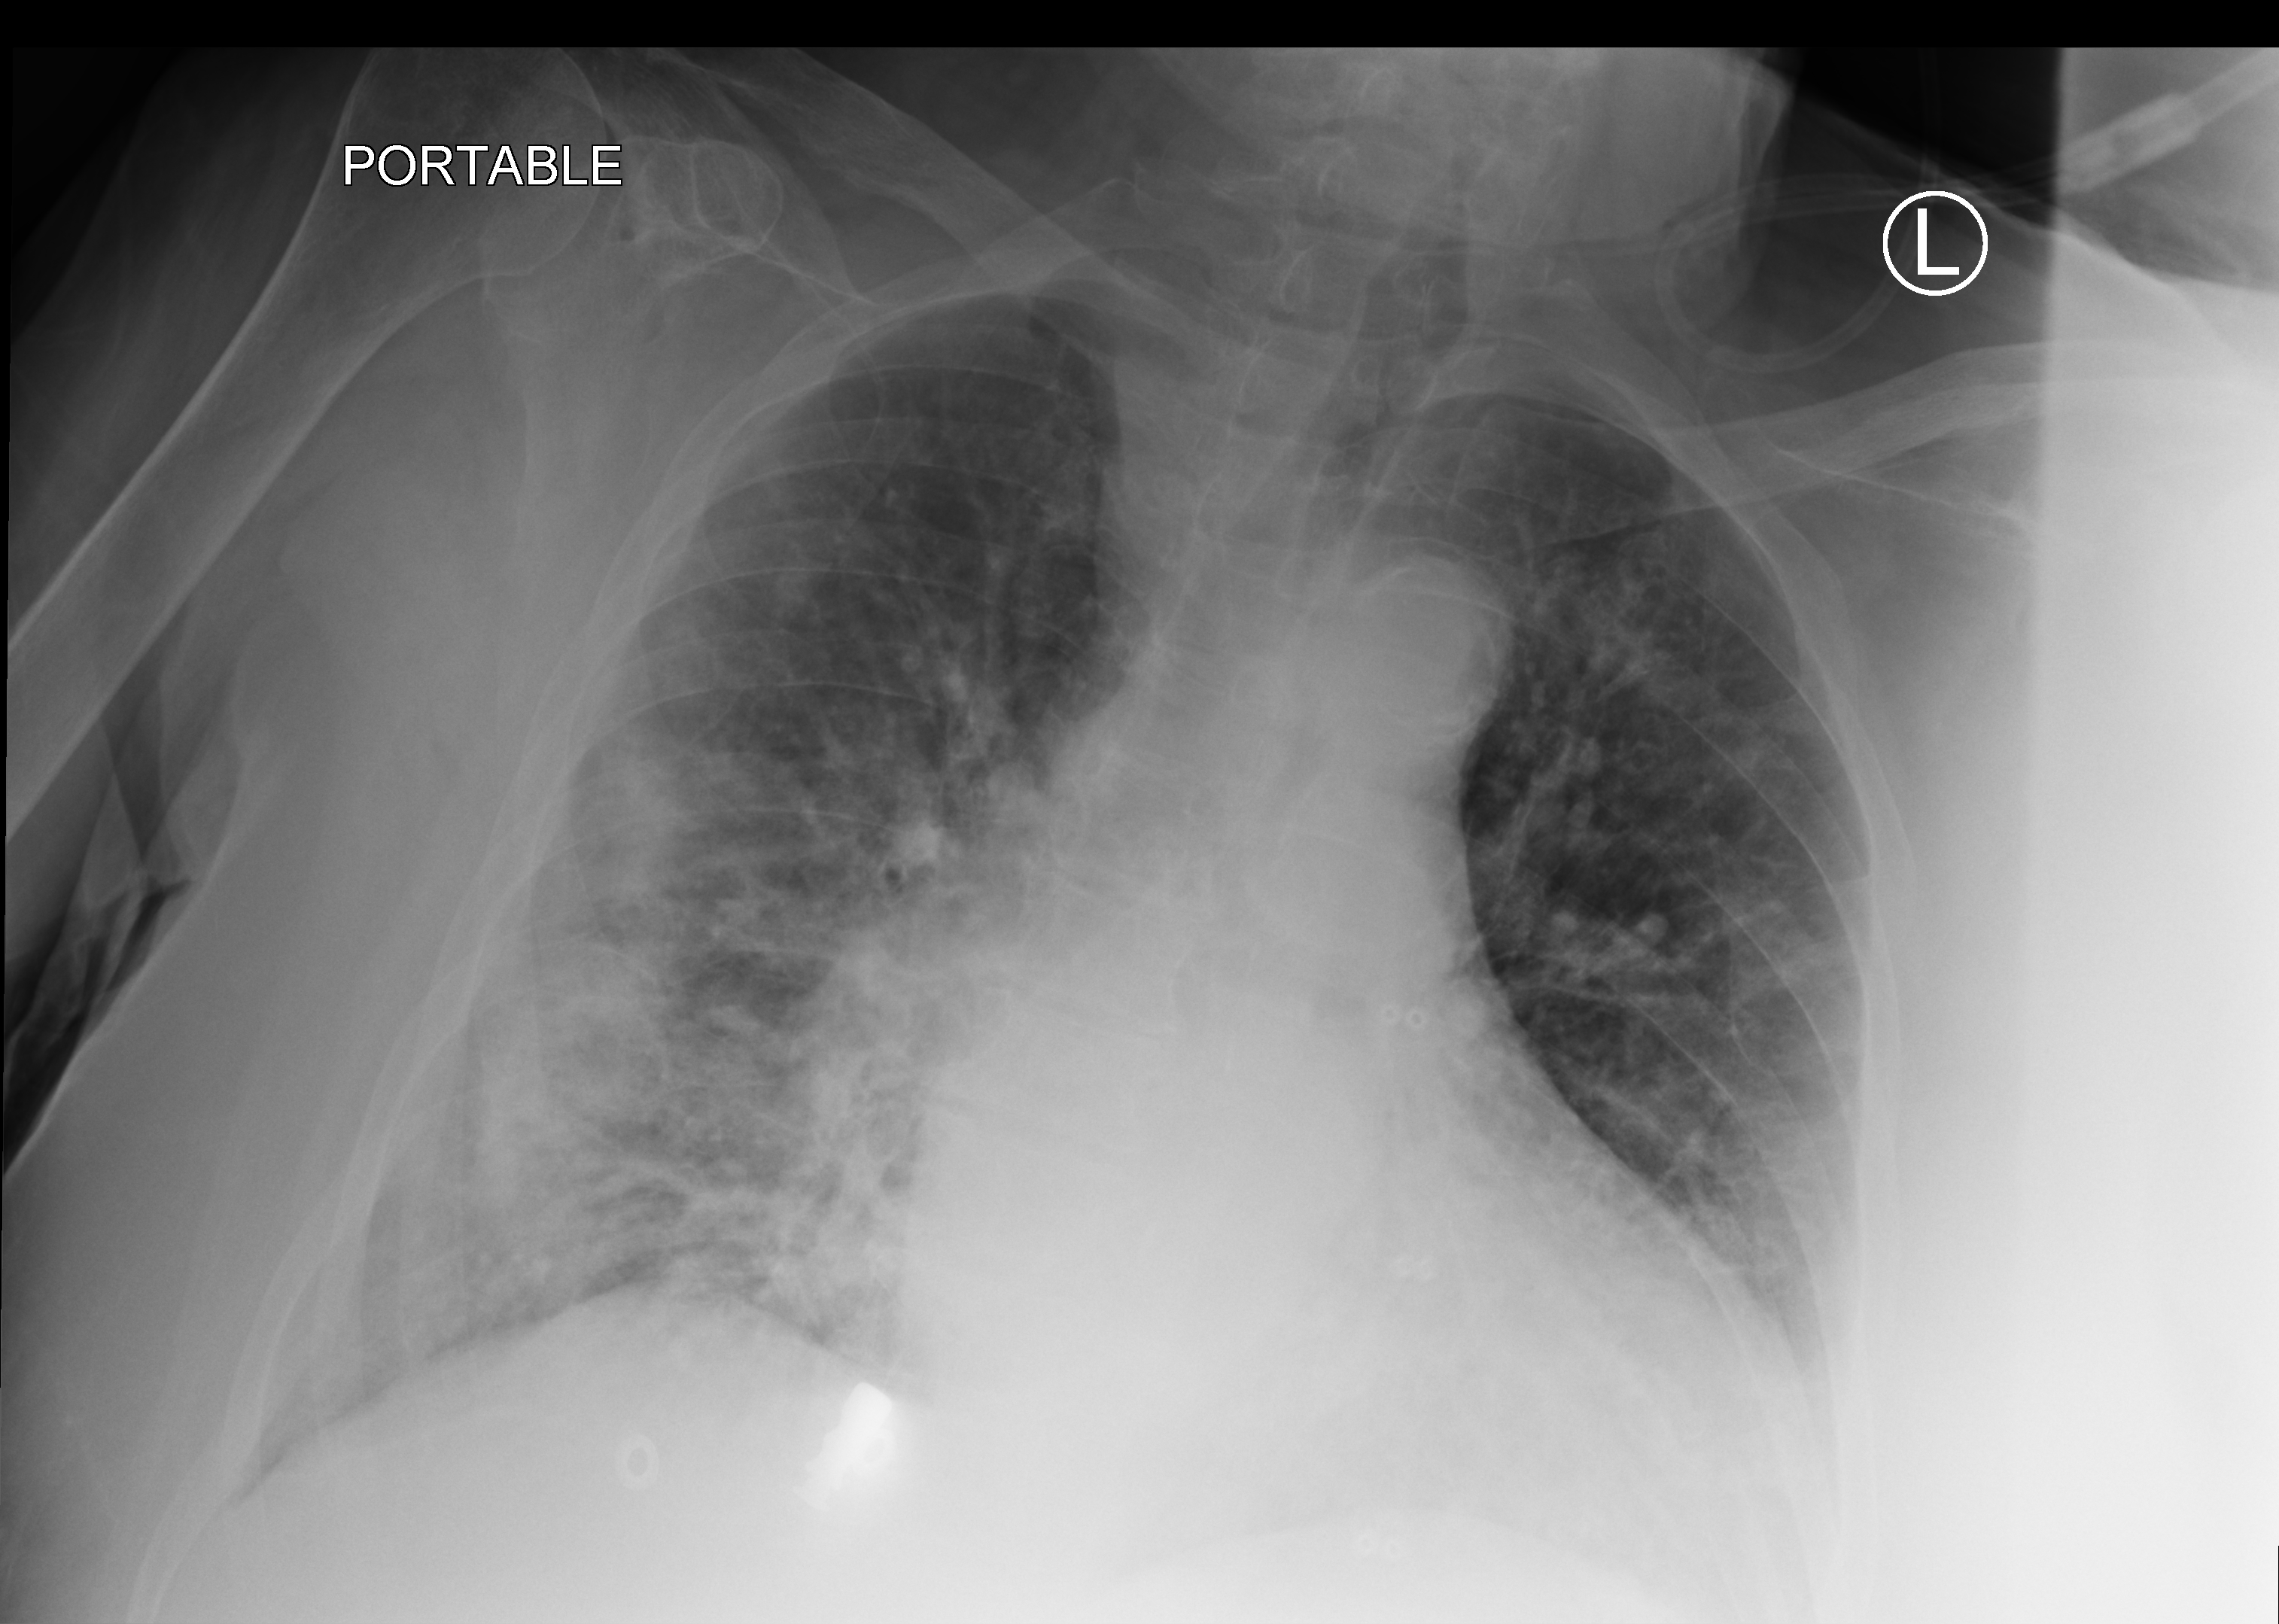
Portable chest radiograph. Patient hospitalised with COVID-19; female, aged 75–90 years.
Admission-level facts for this patient (not findings on this image; timing relative to this image not recorded):
- admitted to intensive care during this hospital stay: no
- mechanically ventilated during this hospital stay: no
- length of hospital stay: 8 days